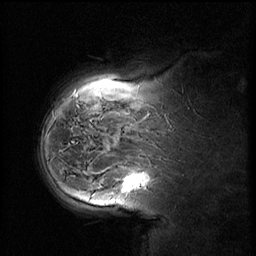
Breast MRI (dynamic contrast-enhanced), one sagittal slice; slice 44 of 58 in the series (ordered by position); dynamic contrast-enhanced series, image 2 of 2 at this slice position (ordered by acquisition); 1.5 T; TE 4.2 ms, TR 8.9 ms; 3 mm slice thickness; 256 × 256 image matrix, field of view 220 × 220 mm. Female patient, age 37 years. Case-level facts recorded for this patient, not image findings: setting: breast cancer imaged before/during neoadjuvant chemotherapy; receptor status: triple-negative.
Annotated regions visible in this slice (semi-automatically segmented with operator editing):
- analysis volume of interest (the breast-tissue region the enhancement analysis was run in; not a lesion): box from (x=114, y=160) to (x=166, y=207) px
- tumour enhancement mask (voxels above the 140 % enhancement threshold inside the analysis volume of interest): (x=124, y=174)–(x=150, y=191)